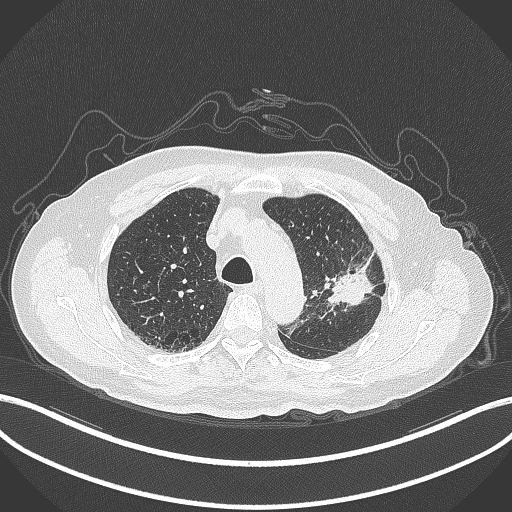
Chest CT, one axial slice; position 224 of 331 along the scan axis; reconstruction kernel B70f; 120 kVp; lung window (W 1500 / L -600 HU); 1 mm slice thickness; 512 × 512 image matrix, field of view 400 × 400 mm. Patient: male, 79 years. From the clinical record (not read from this slice): clinical TNM (as recorded): T2a N1 M1.
Annotated regions visible in this slice (rectangle marked by the reading radiologist):
- lung tumour (recorded histology: adenocarcinoma): bounding box [x1, y1, x2, y2] px = [328, 246, 387, 310]